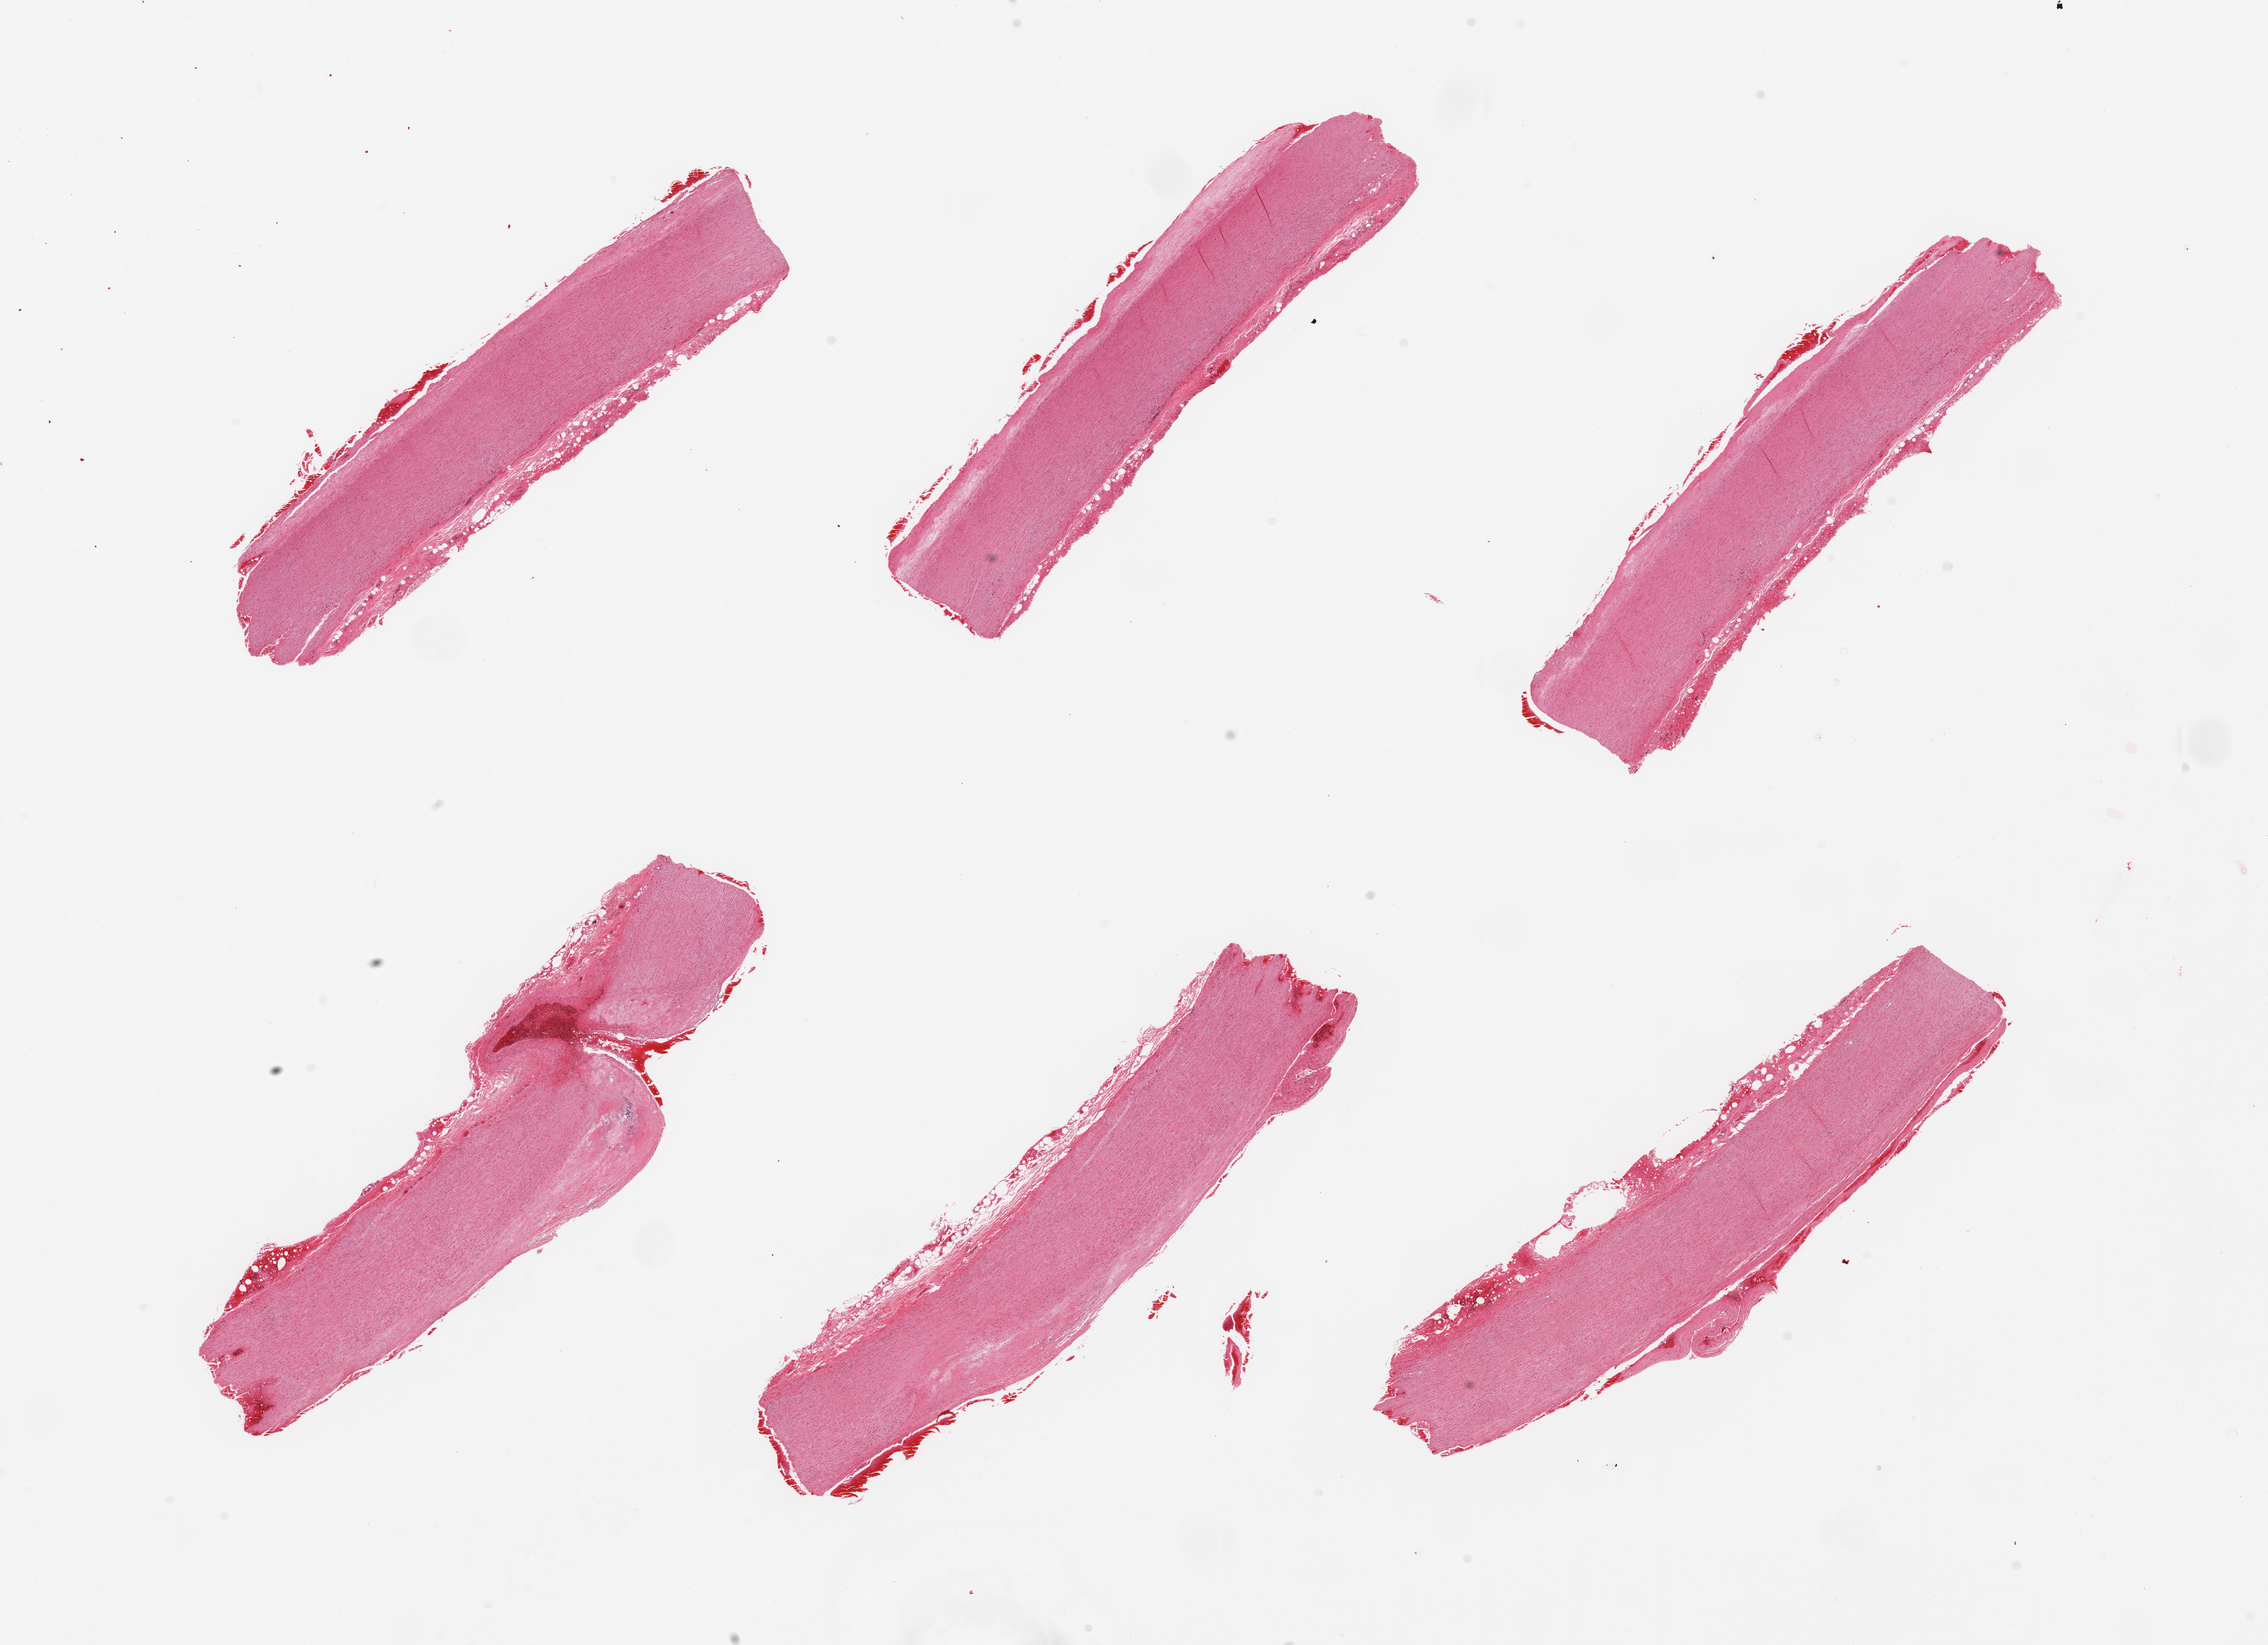
H&E whole-slide image, a low-resolution overview of the entire scanned area, about 25.6 x 18.6 mm (from a 20x scan); PAXgene-fixed, paraffin-embedded tissue; target tissue: aorta; tissue donor sample.
Reviewer comment on this tissue sample: 6 pieces; calcific atherosclerosis.